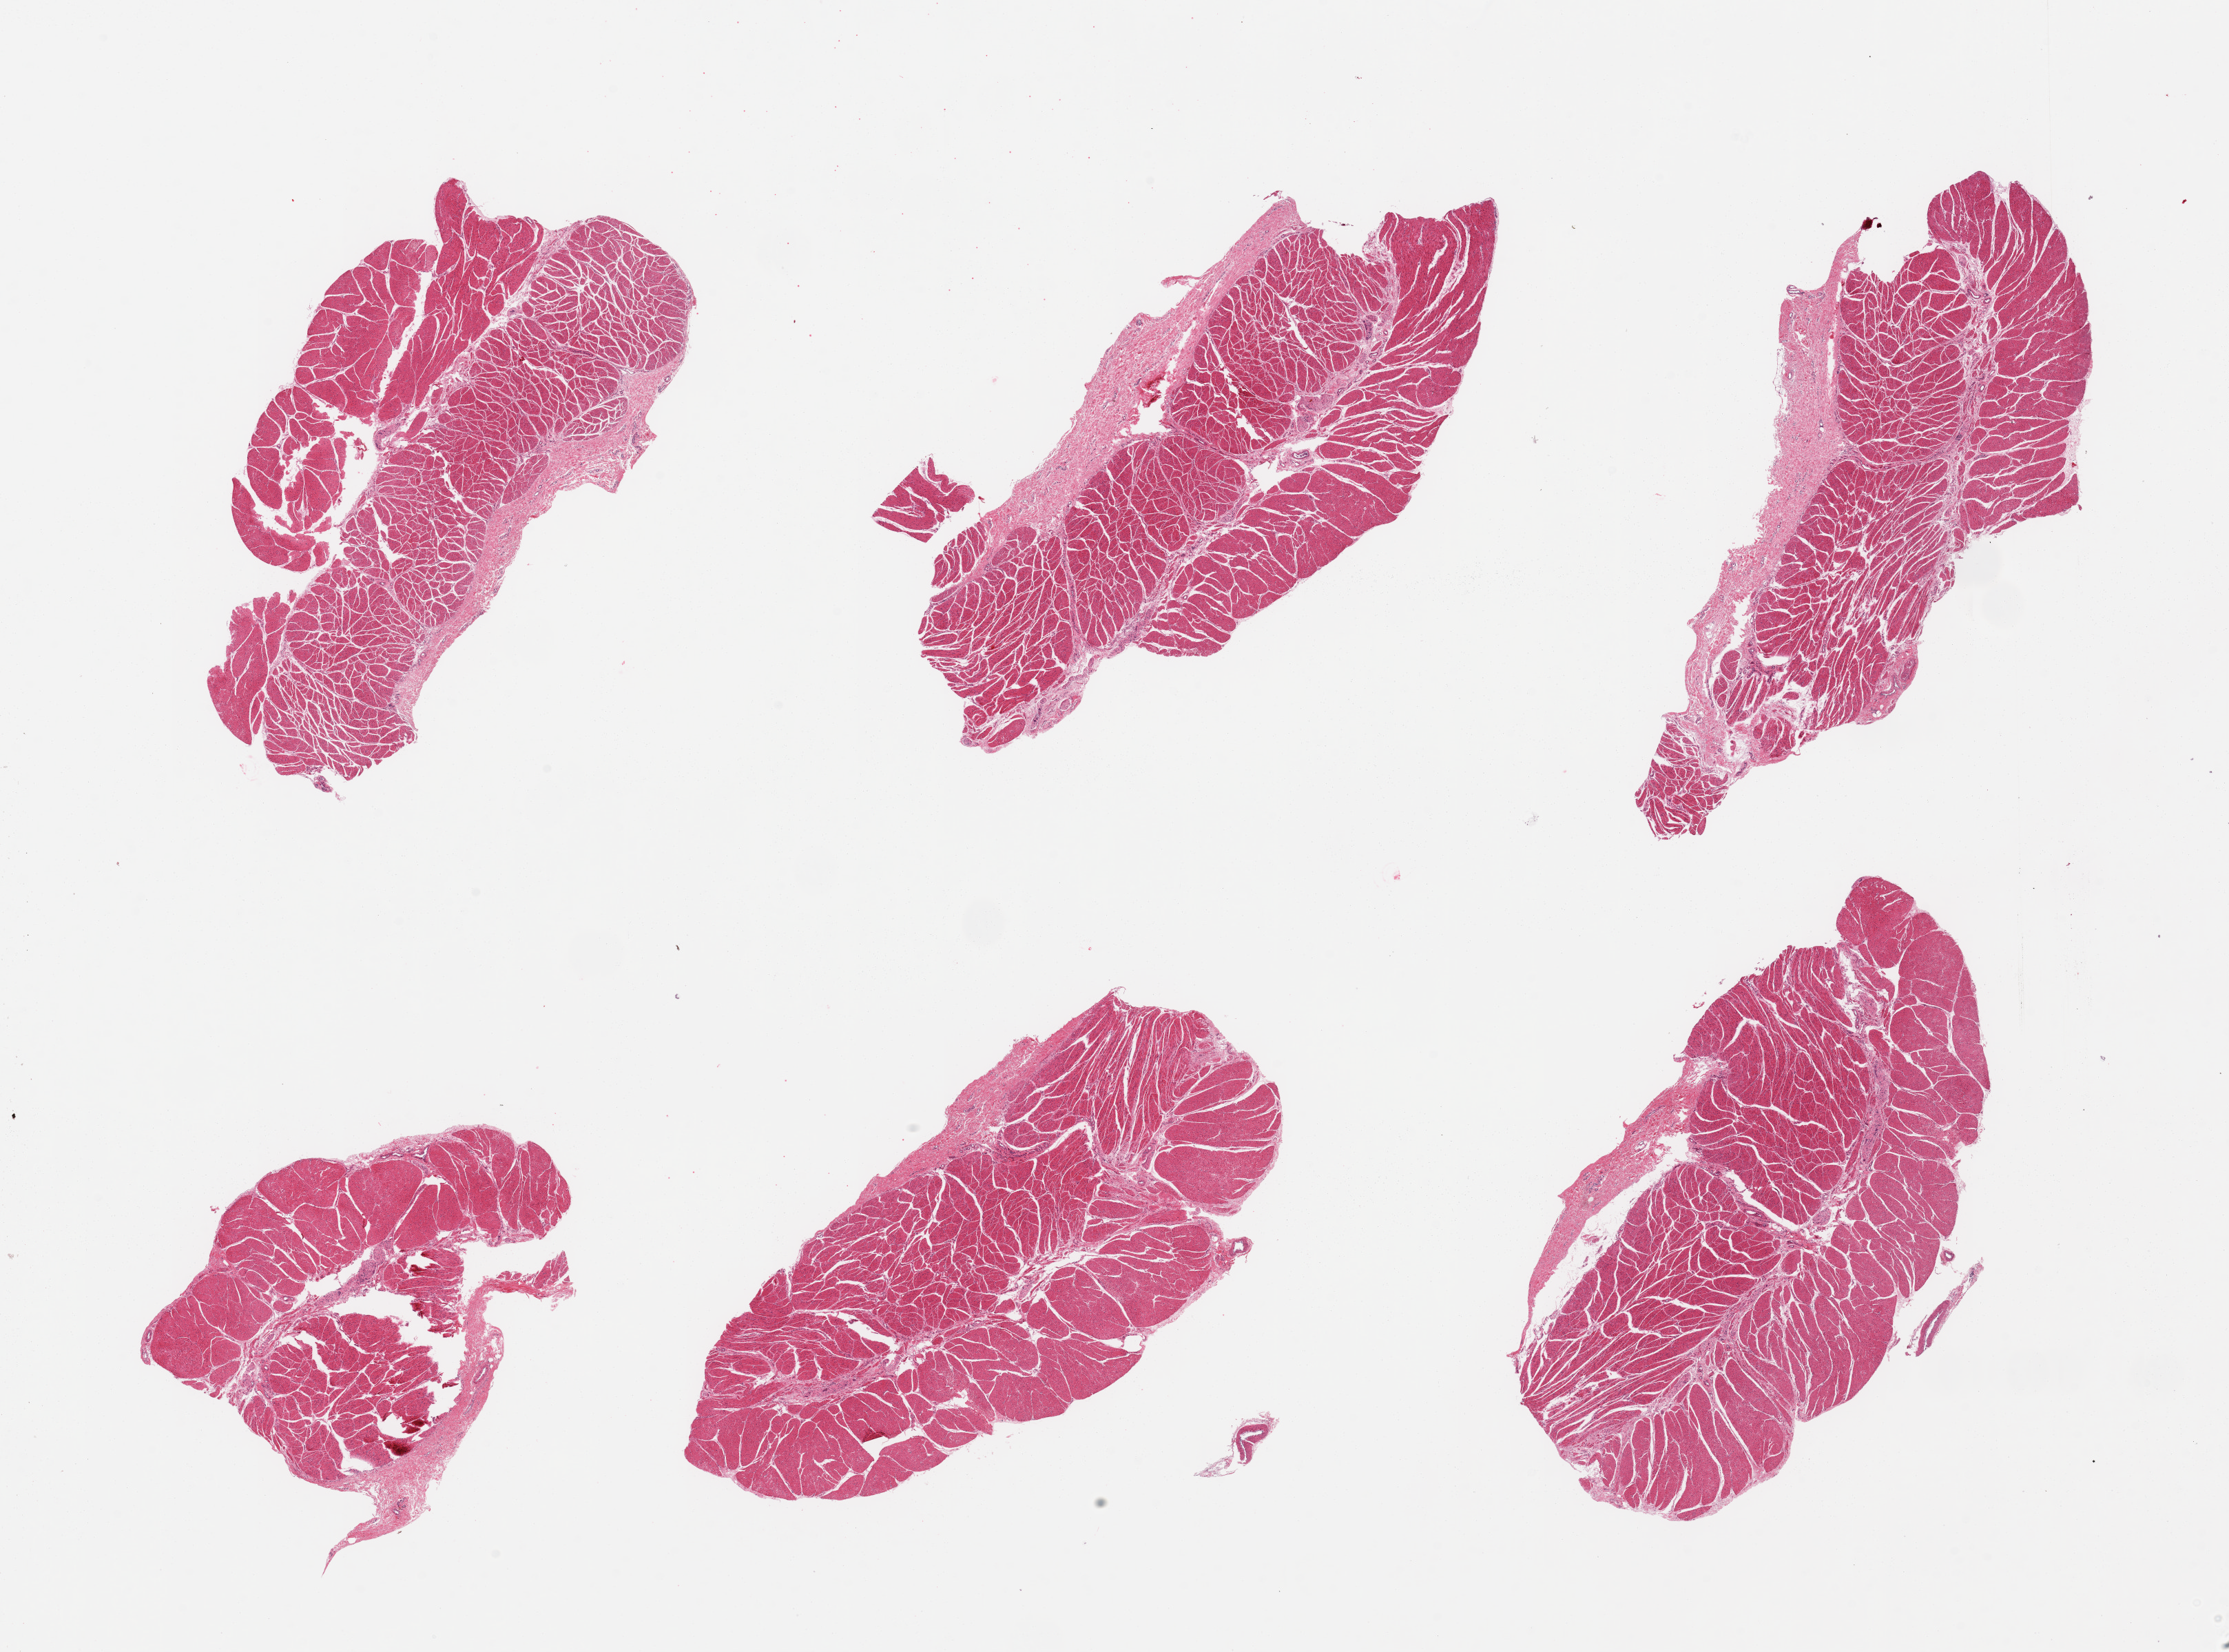
Haematoxylin and eosin whole-slide image, brightfield — shown as a low-resolution overview of the whole scanned area (about 25.6 x 19.0 mm); PAXgene-fixed, paraffin-embedded tissue; sampled site (target tissue): esophageal muscle; tissue donor sample. Male donor.
Reviewer comment on this tissue sample: 6 pieces; well dissected muscle with thin [0.6mm] layer of submucosal stroma.